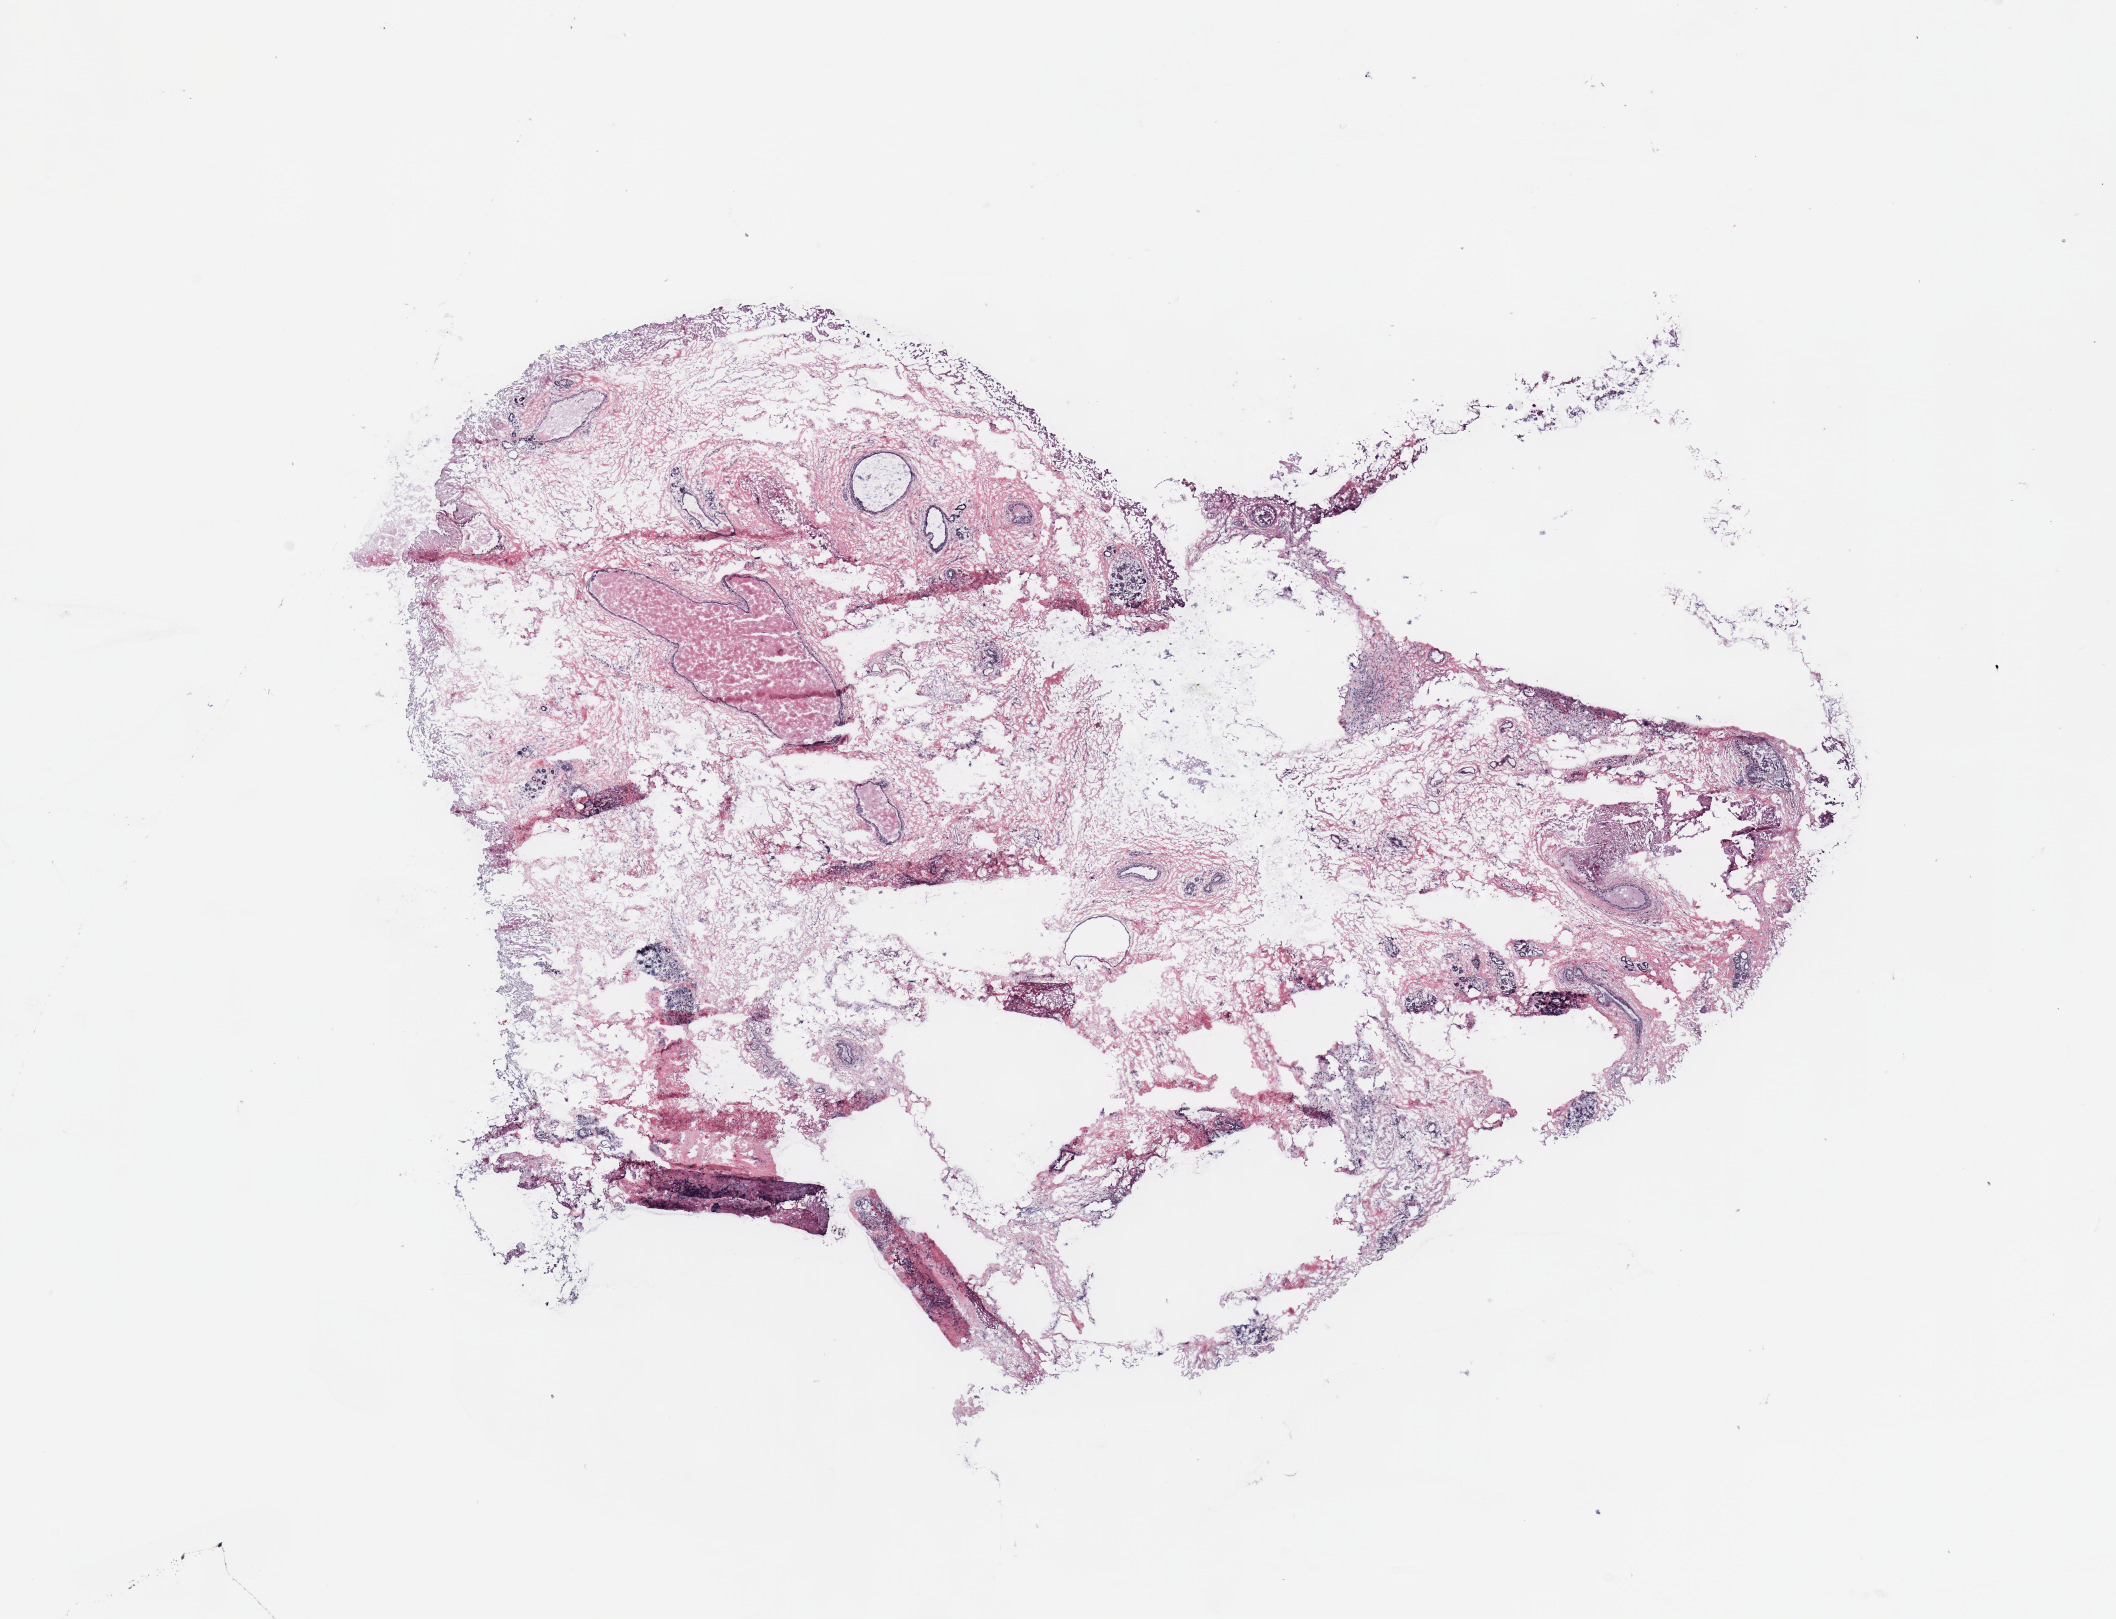
Digitized H&E-stained tissue section (whole slide) — shown as a low-resolution overview of the whole scanned area (about 16.7 x 12.8 mm, slide scanned at 20x). Tumour tissue sample, breast. Patient: female, age 54 years.
Histologic diagnosis: Infiltrating lobular carcinoma, NOS.